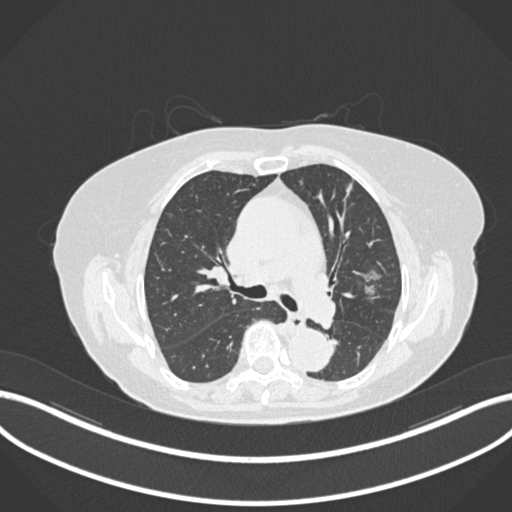
Chest CT, one axial slice; slice 98 of 168 in the series (ordered by position); reconstruction kernel B30f; 120 kVp; lung window (W 1500 / L -600 HU); 512 × 512 image matrix. Patient: female, 75 years. From the clinical record (not read from this slice): clinical TNM (as recorded): T1c N0 M0.
Outlined on this slice (bounding box drawn by a radiologist):
- lung tumour (recorded histology: adenocarcinoma): bounding box (x1, y1, x2, y2) in pixels: (354, 270, 383, 301)